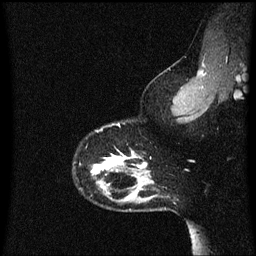
Breast MRI (dynamic contrast-enhanced), one sagittal slice. Position 50 of 60 along the scan axis. Dynamic contrast-enhanced series, image 2 of 3 at this slice position (ordered by acquisition). 1.5 T. TE 4.2 ms, TR 8.4 ms. 256 × 256 image matrix, field of view 200 × 200 mm. Patient: female, 33 years.
Structures marked on this image (semi-automatic segmentation, software-assisted and operator-edited):
- analysis volume of interest (the breast-tissue region the enhancement analysis was run in; not a lesion): bounding box <74,126,152,191> (left, top, right, bottom; pixels)
- tumour enhancement mask (voxels above the 70 % enhancement threshold inside the analysis volume of interest): <92,150,148,175>